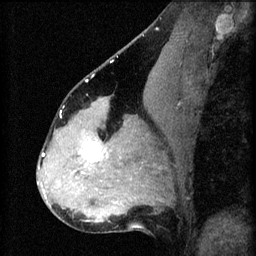
Breast MRI (dynamic contrast-enhanced), one sagittal slice; 3 images stored at this slice position (order not interpretable as contrast timing); 1.5 T; TE 4.2 ms, TR 8.2 ms; 2.3 mm slice thickness; 256 × 256 image matrix. Female patient, age 37 years.
Outlined on this slice (semi-automatic segmentation, software-assisted and operator-edited):
- analysis volume of interest (the breast-tissue region the enhancement analysis was run in; not a lesion): bounding box (x1, y1, x2, y2) in pixels: (67, 120, 122, 179)
- tumour enhancement mask (voxels above the 70 % enhancement threshold inside the analysis volume of interest): (84, 142, 102, 163)